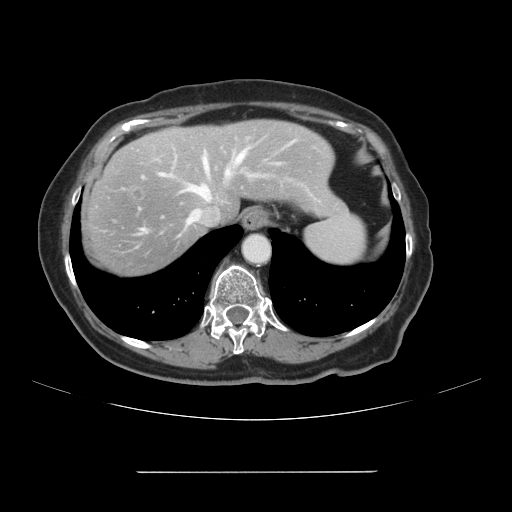
Contrast-enhanced abdominal CT, one axial slice; position 88 of 111 along the scan axis; 120 kVp; soft-tissue window (W 400 / L 40 HU); 512 × 512 image matrix, field of view 400 × 400 mm. Female patient, age 74 years. From the clinical record (not read from this slice): diagnosis: colorectal cancer liver metastases, imaged before liver resection; multiple liver metastases: yes; largest metastasis: 1.1 cm; chemotherapy before resection: yes.
Annotated regions visible in this slice (outlined manually by an expert reader):
- hepatic veins: box from (x=143, y=138) to (x=299, y=231) px
- liver: (x=81, y=120)–(x=343, y=278)
- planned liver remnant (the part of the liver to remain after resection): (x=169, y=120)–(x=344, y=218)
- portal vein (with intrahepatic branches): (x=183, y=163)–(x=233, y=192)
- liver metastasis: (x=130, y=189)–(x=145, y=201)